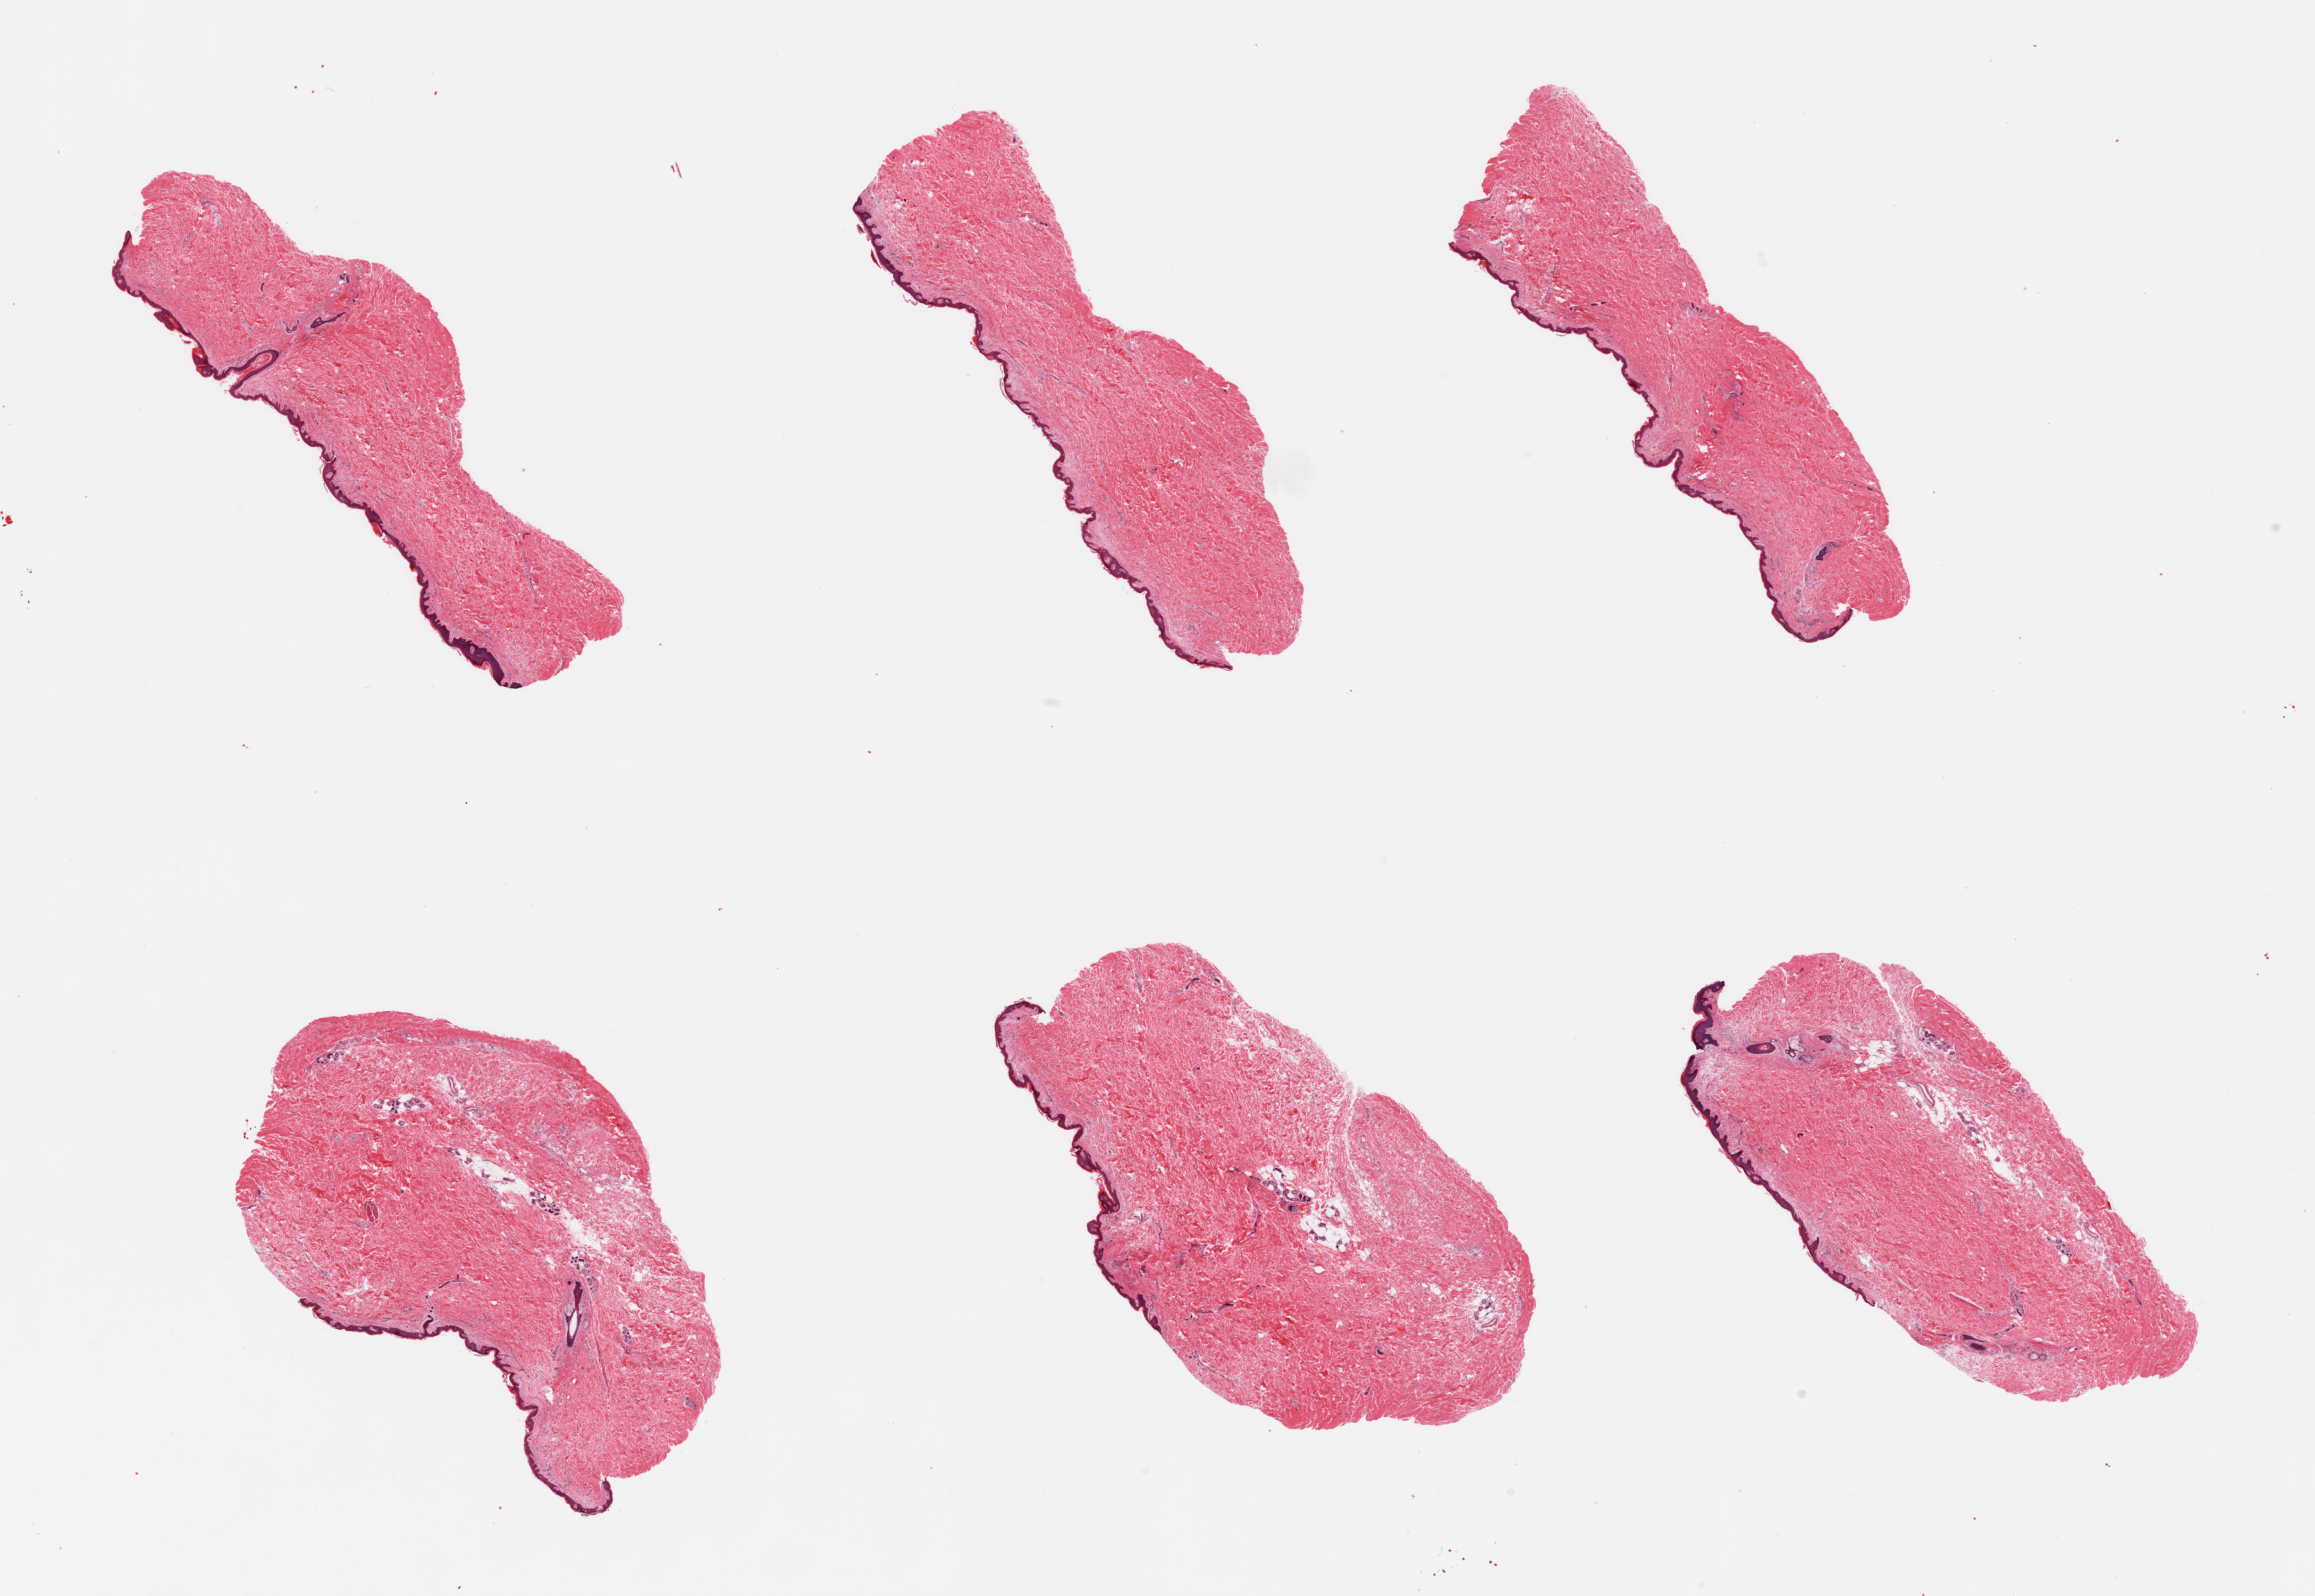
Whole-slide image, haematoxylin and eosin stain, brightfield, shown as a low-resolution overview of the whole scanned area (about 28.5 x 19.7 mm, acquisition: 20x scan); PAXgene-fixed paraffin-embedded (PFPE) section; target tissue: skin of suprapubic region; donor tissue sample. Male donor.
Reviewer comment on this tissue sample: 6 pieces, no dermal fat, squamous epithelium is ~50 microns.